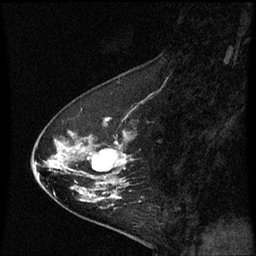
Breast MRI (dynamic contrast-enhanced), one sagittal slice. Position 21 of 60 along the scan axis. Dynamic contrast-enhanced series, image 2 of 3 at this slice position (ordered by acquisition). 1.5 T. TE 4.2 ms, TR 8.9 ms. 2 mm slice thickness. 256 × 256 image matrix. Female patient, age 53 years. From the clinical record (not read from this slice): setting: breast cancer imaged before/during neoadjuvant chemotherapy; receptor status: HR-positive, HER2-negative.
Structures marked on this image (semi-automatically segmented with operator editing):
- analysis volume of interest (the breast-tissue region the enhancement analysis was run in; not a lesion): bounding box <32,102,143,221> (left, top, right, bottom; pixels)
- tumour enhancement mask (voxels above the 70 % enhancement threshold inside the analysis volume of interest): <56,120,127,197>